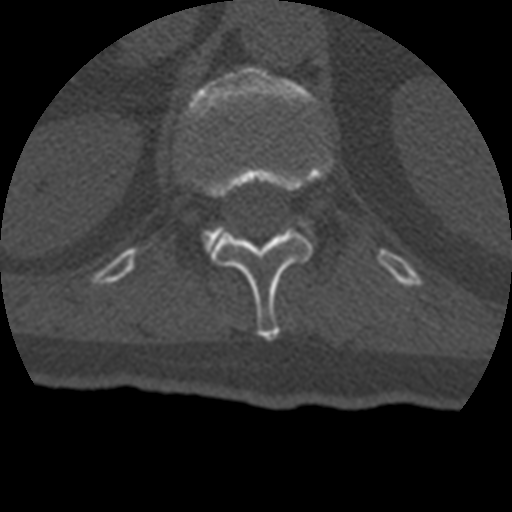
CT including the spine, one axial slice; position 163 of 399 along the scan axis; reconstruction kernel STANDARD; bone window (W 1800 / L 400 HU); 1.25 mm slice thickness; 512 × 512 image matrix. Patient age 69 years. Case-level facts recorded for this patient, not image findings: primary cancer: prostate.
Outlined on this slice (semi-automatic segmentation, software-assisted and operator-edited):
- L1 vertebra: bounding box [x1, y1, x2, y2] px = [184, 66, 317, 253]
- T12 vertebra: [208, 161, 331, 340]